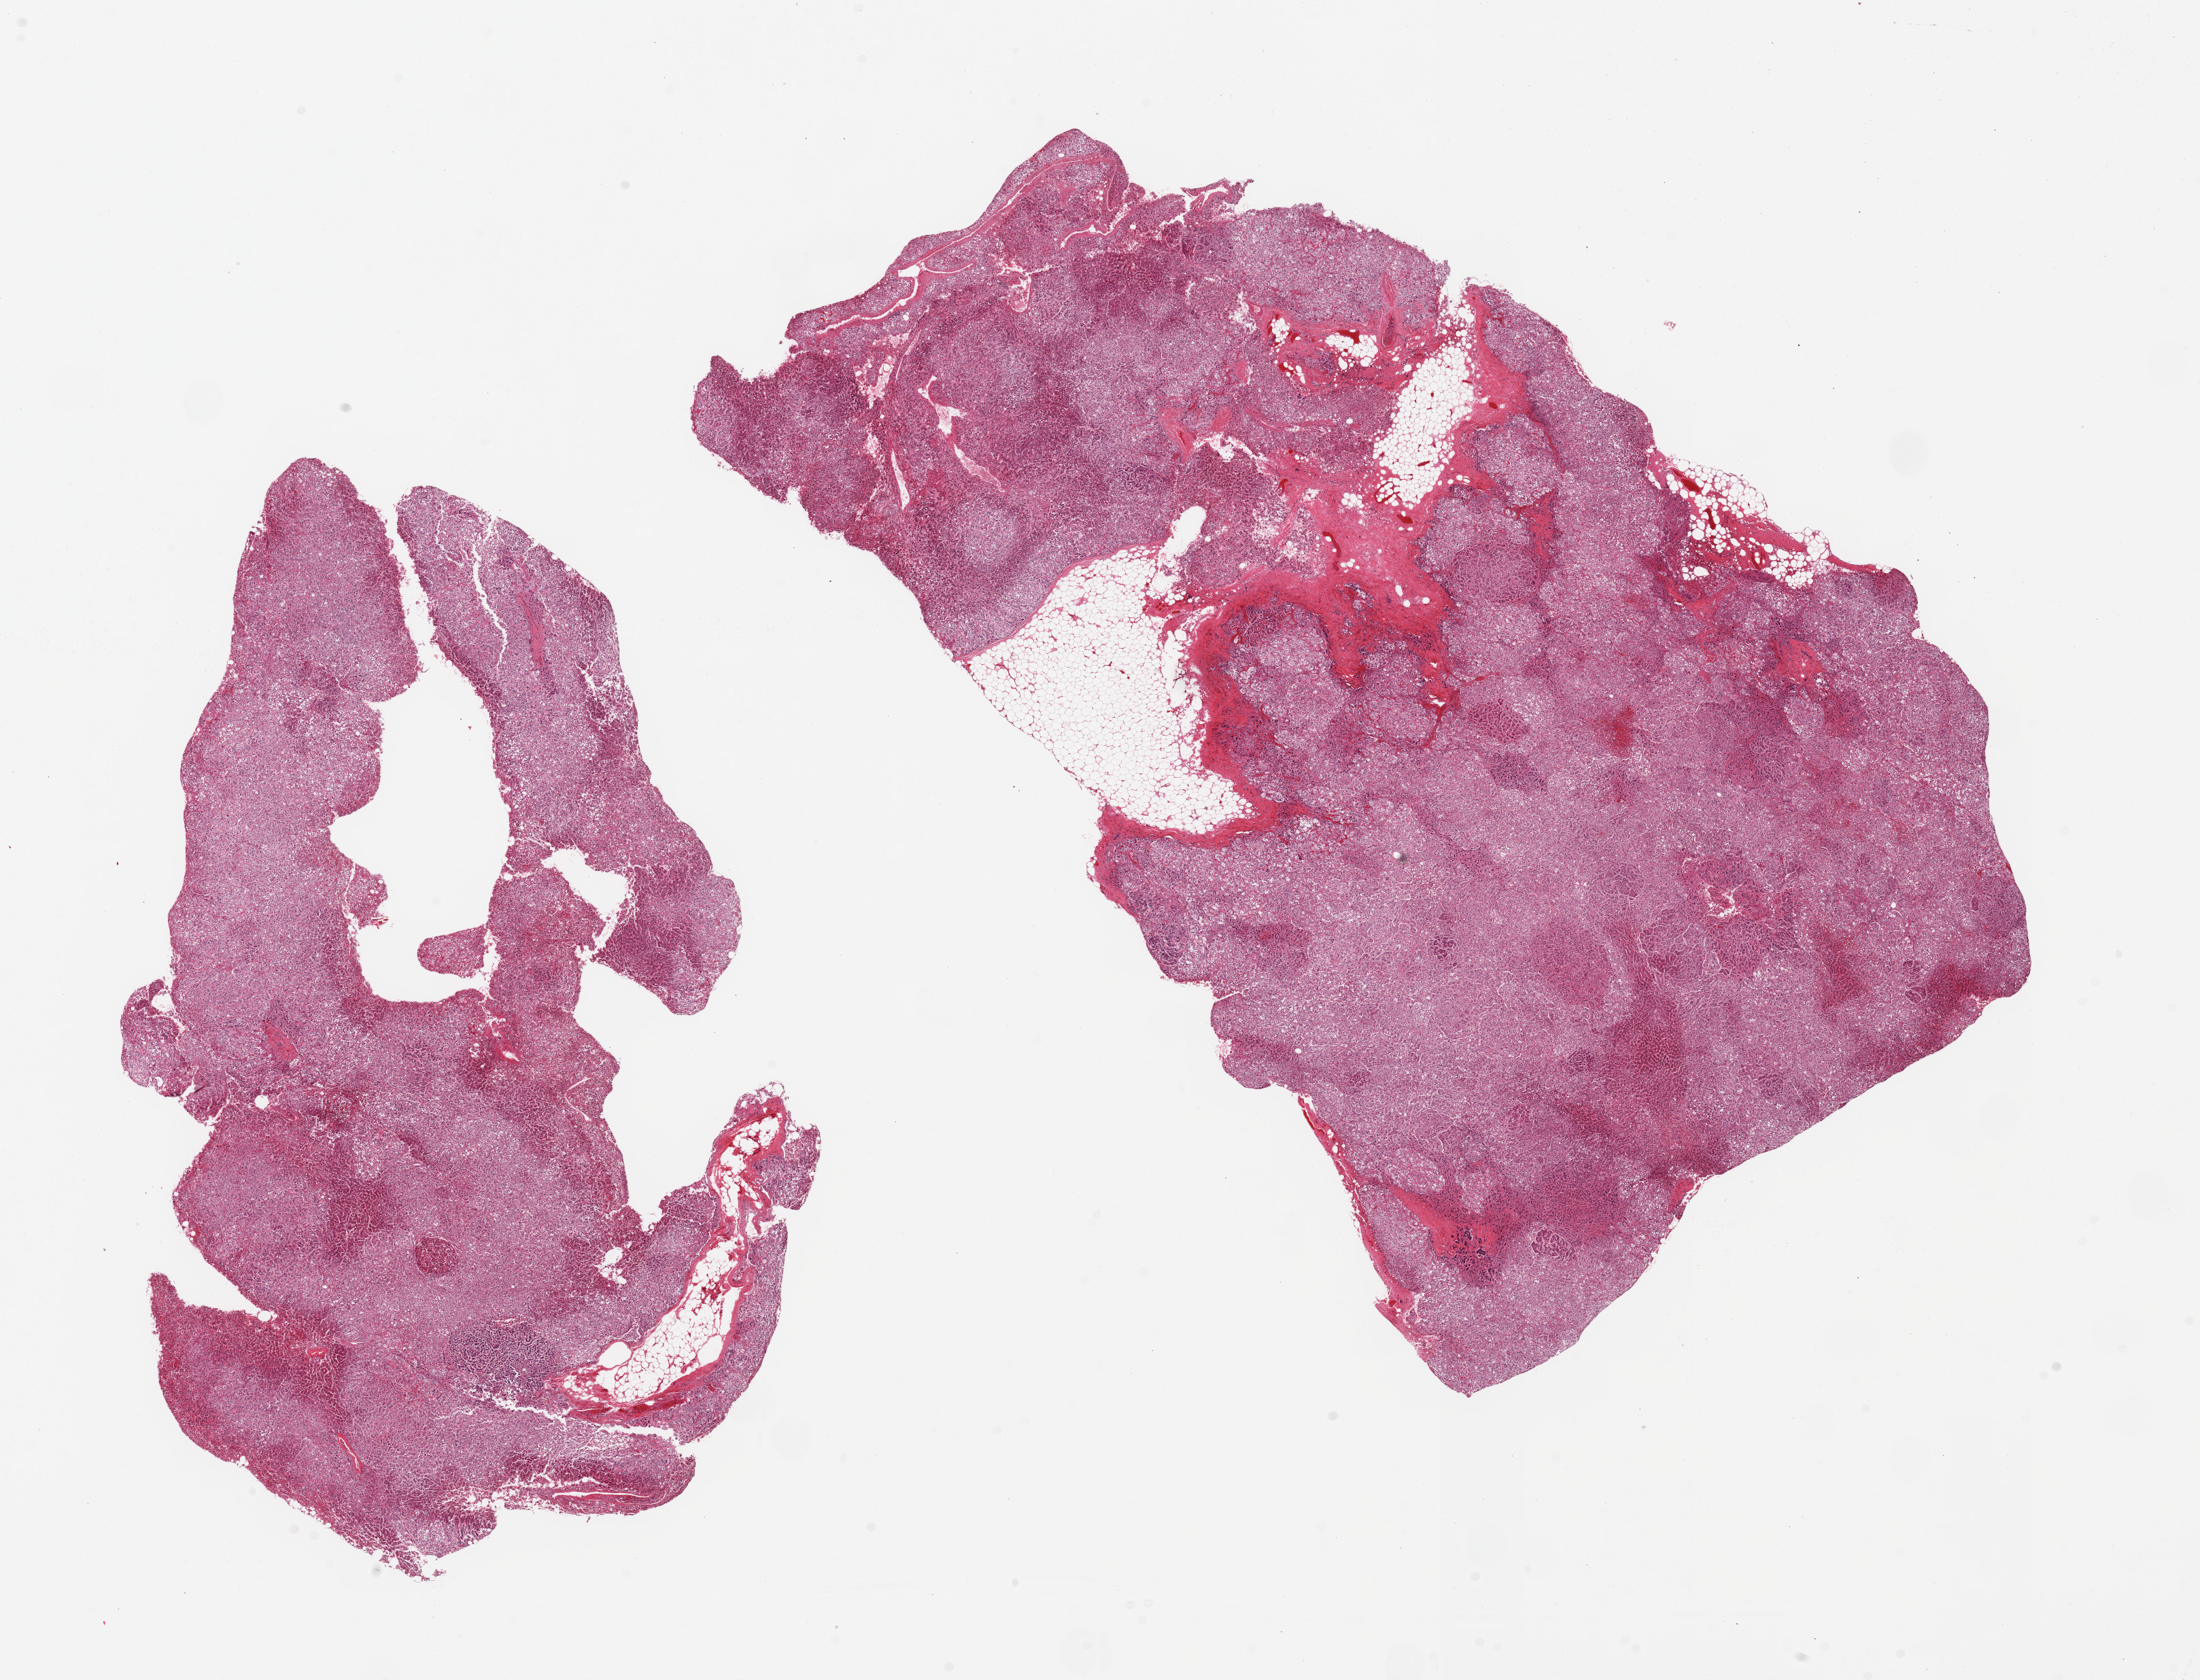
Whole-slide image, haematoxylin and eosin stain, shown as a low-resolution overview of the whole scanned area (about 25.6 x 19.5 mm, acquisition: 20x scan). PAXgene-fixed paraffin-embedded (PFPE) section. Target tissue: adrenal gland. Tissue donor sample. Donor: male.
- review note (as recorded): 2 pieces; cortex; 10% internal fat